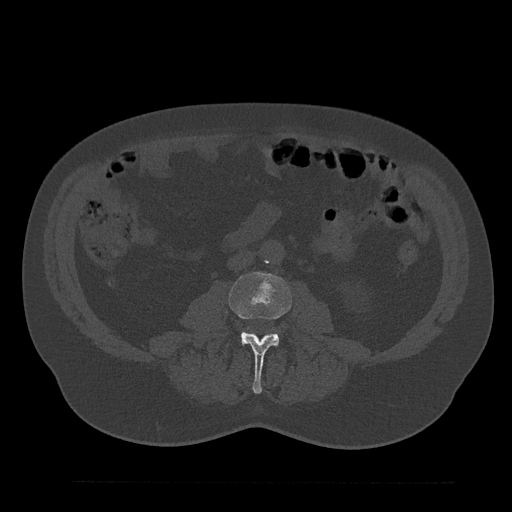
CT including the spine, one axial slice. Slice 18 of 797 in the series (ordered by position). Reconstruction kernel Br40s/3. Bone window (W 1800 / L 400 HU). 0.5 mm slice thickness. 512 × 512 image matrix, field of view 430 × 430 mm. Male patient, age 61 years. Case-level facts recorded for this patient, not image findings: primary cancer: prostate.
Structures marked on this image (semi-automatic segmentation, software-assisted and operator-edited):
- L3 vertebra: bounding box [x1, y1, x2, y2] px = [228, 272, 292, 394]